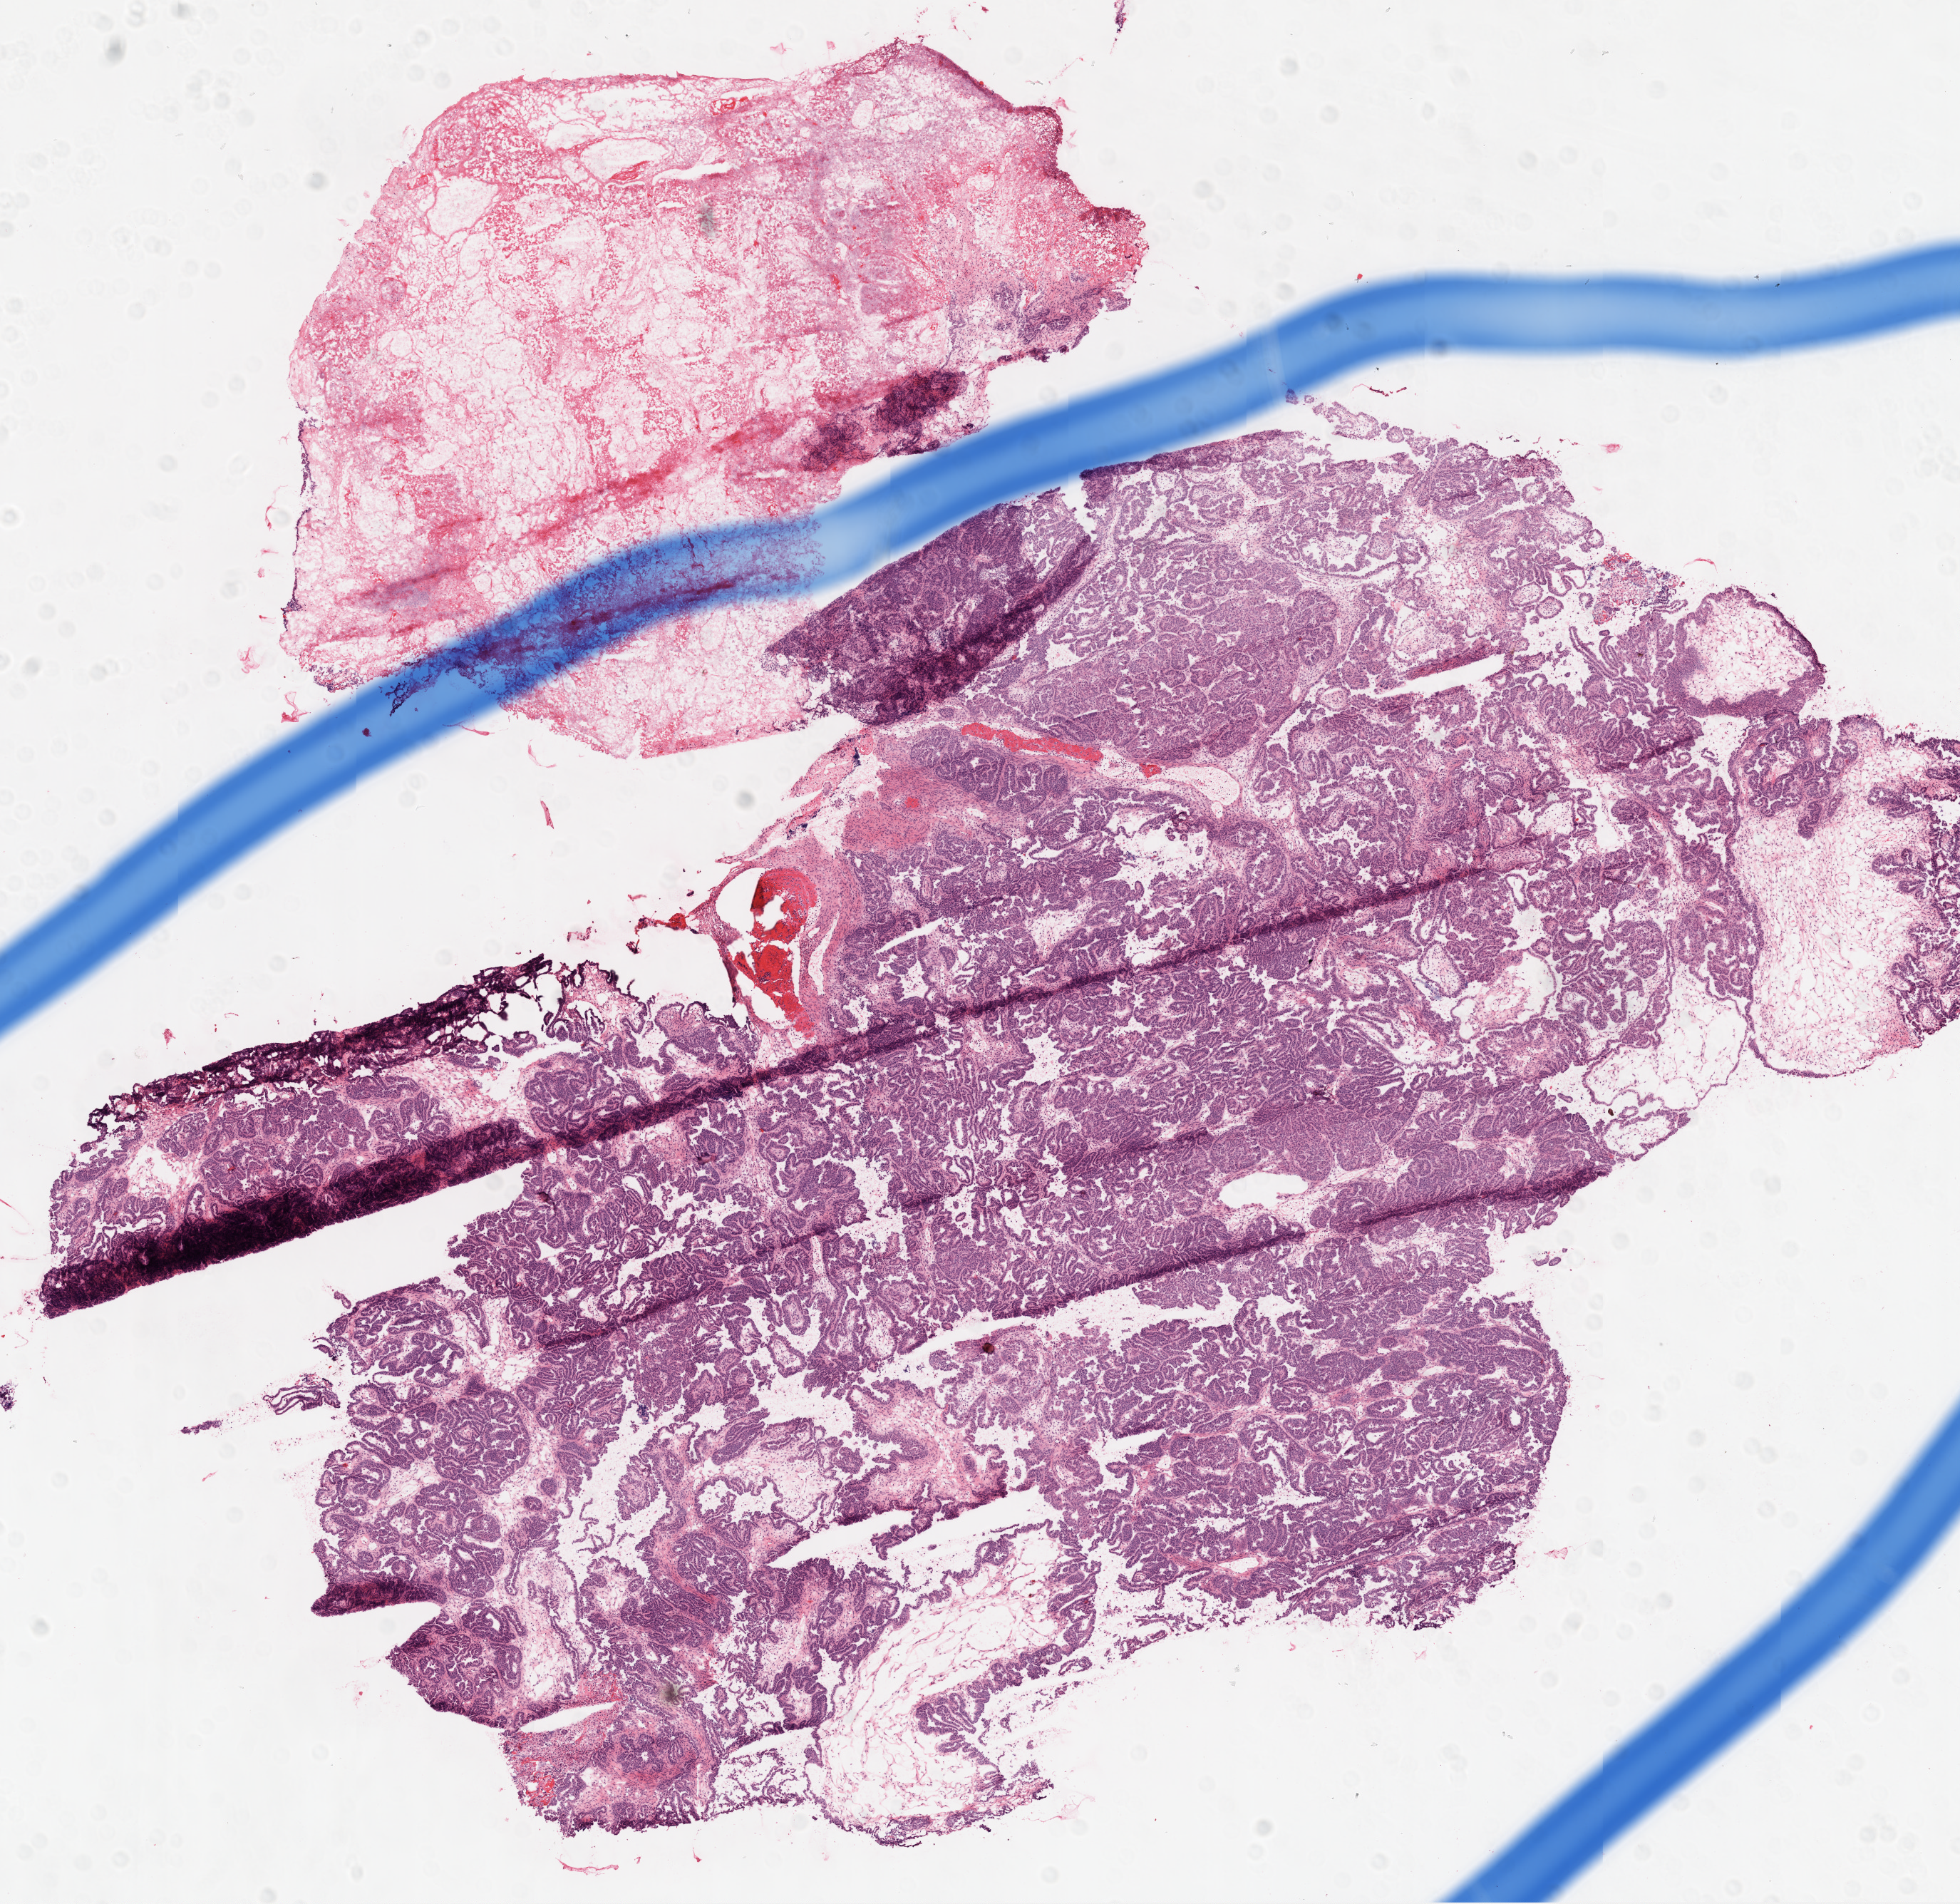
Whole-slide histology image, H&E, shown as a low-resolution overview of the whole scanned area (about 11.0 x 10.7 mm); frozen section from the top of the tissue portion; primary tumour sample from the ovary. Female, age 59 years at initial diagnosis. Histologic grade: G2 (moderately differentiated). Composition of this section per pathologist review: tumour cells 75%, tumour nuclei 85%, normal cells 0%, stromal cells 5%, necrosis 20%.
- FIGO stage: IV
- laterality: bilateral
- pathologic diagnosis: Serous cystadenocarcinoma, NOS